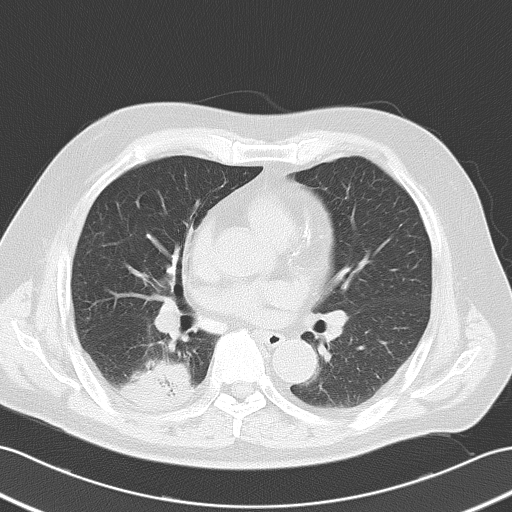
Chest CT, one axial slice; position 22 of 52 along the scan axis; reconstruction kernel B70f; 120 kVp; lung window (W 1500 / L -600 HU); 512 × 512 image matrix. Male patient, age 70 years. From the clinical record (not read from this slice): clinical TNM (as recorded): T2 N0 M0; histopathological grade: G2.
Outlined on this slice (rectangle marked by the reading radiologist):
- lung tumour (recorded histology: adenocarcinoma): bounding box [x1, y1, x2, y2] px = [121, 353, 201, 418]